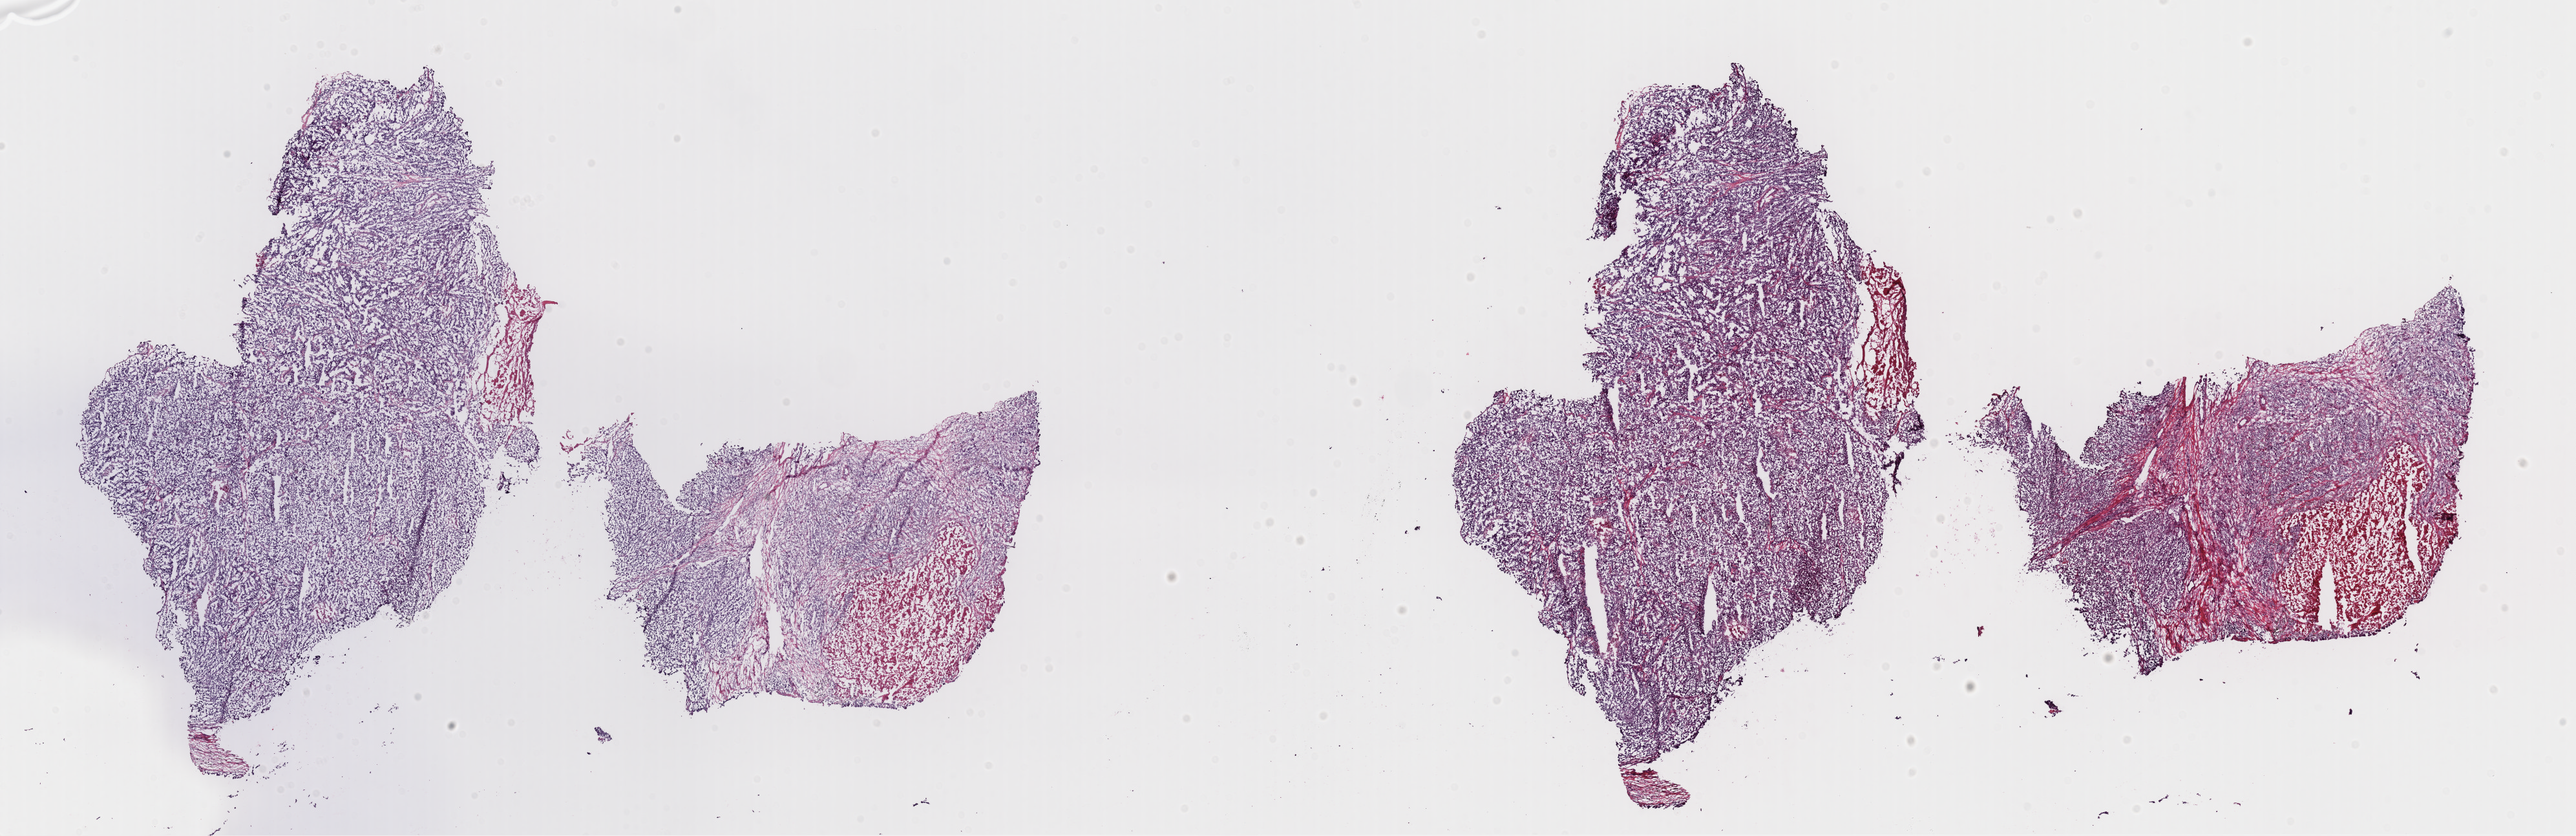
Digitized H&E-stained tissue section (whole slide) — a low-resolution overview of the entire scanned area, about 31.5 x 10.2 mm; frozen section from the top of the tissue portion; metastatic tumour sample. Male, age 65 years at initial diagnosis. Composition of this section per pathologist review: tumour cells 80%, tumour nuclei 90%, normal cells 0%, stromal cells 10%, necrosis 10%. Infiltration values recorded for this section: lymphocyte infiltration 0%, monocyte infiltration 0%, neutrophil infiltration 0%.
- this section: metastatic tumour tissue
- patient diagnosis: Malignant melanoma, NOS